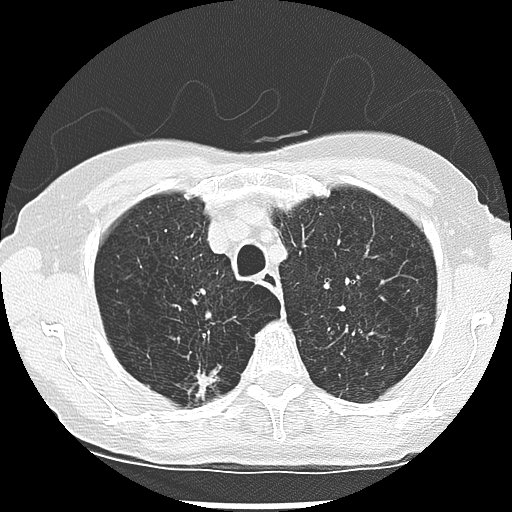
Low-dose screening chest CT, one axial slice; slice 218 of 265 in the series (ordered by position); reconstruction kernel LUNG; lung window (W 1500 / L -600 HU); 2.5 mm slice thickness; 512 × 512 image matrix.
Outlined on this slice (outlined manually by an expert reader):
- lesion 1 (nodule, upper lobe of right lung): bounding box <197,372,217,398> (left, top, right, bottom; pixels)